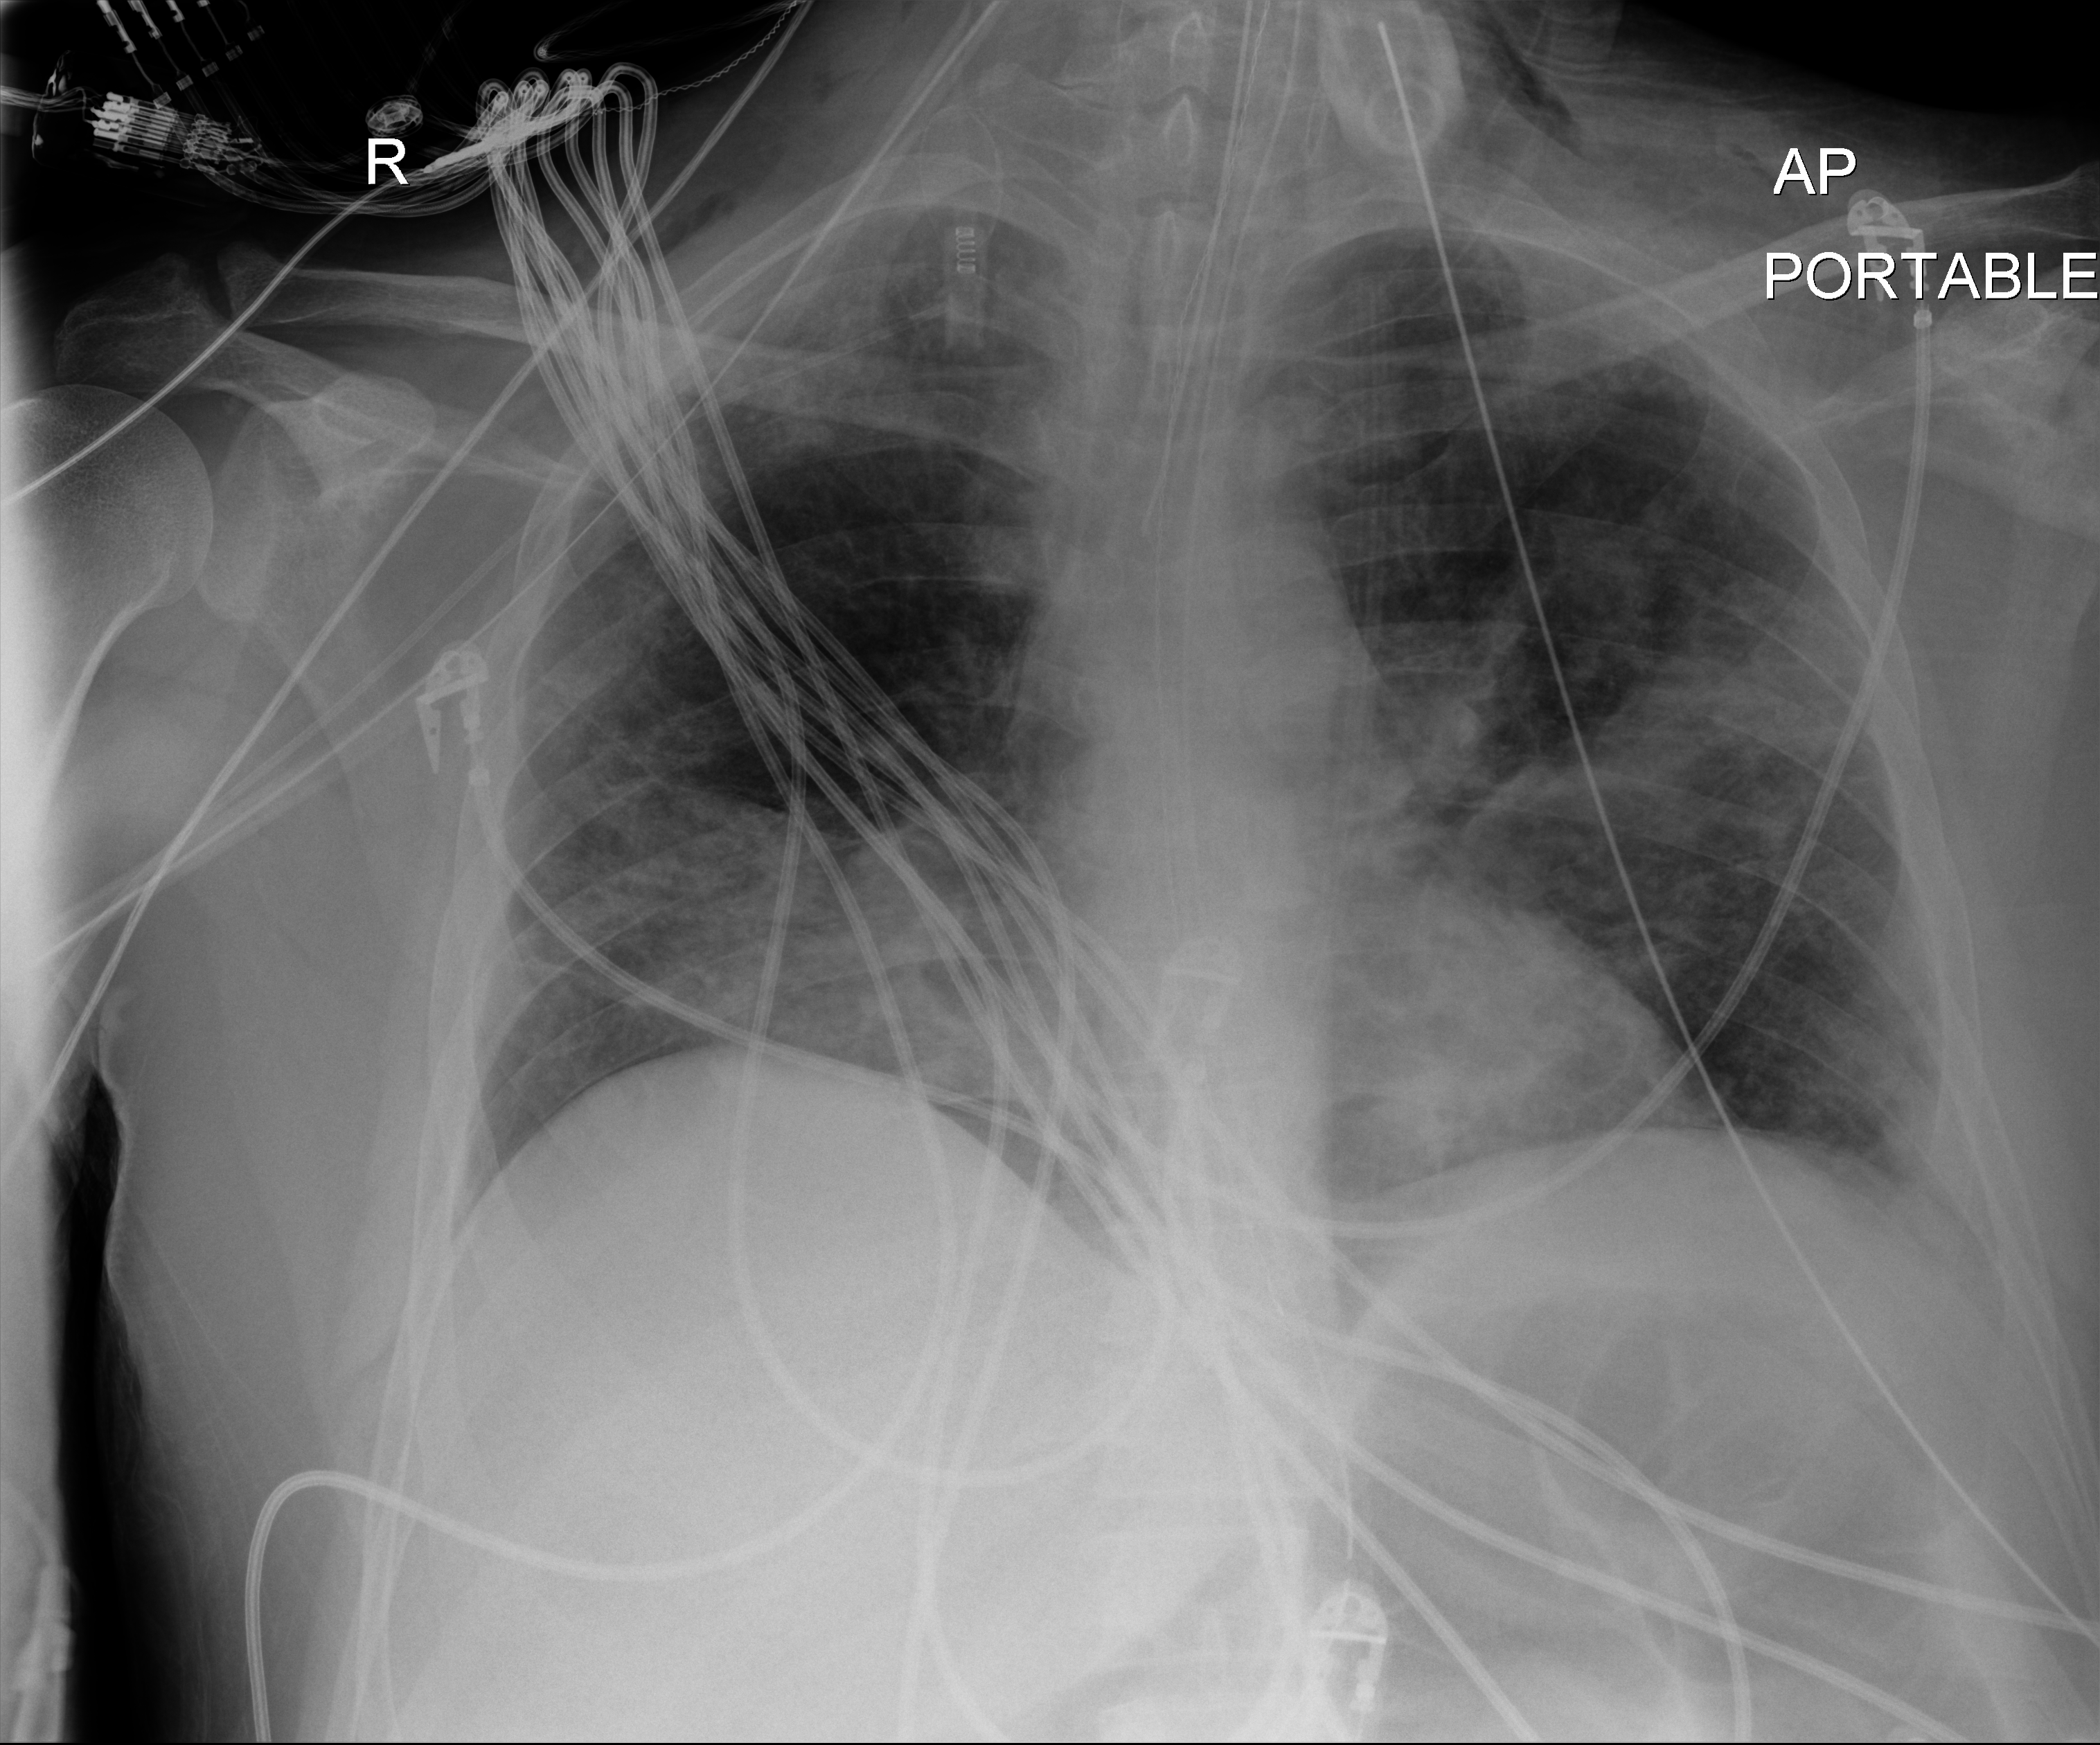
Chest radiograph, anteroposterior (AP) projection. Adult patient hospitalised with COVID-19, age 18–59 years.
Admission-level facts for this patient (not findings on this image; timing relative to this image not recorded): hypertension (admission record): yes; admitted to intensive care during this hospital stay: yes.